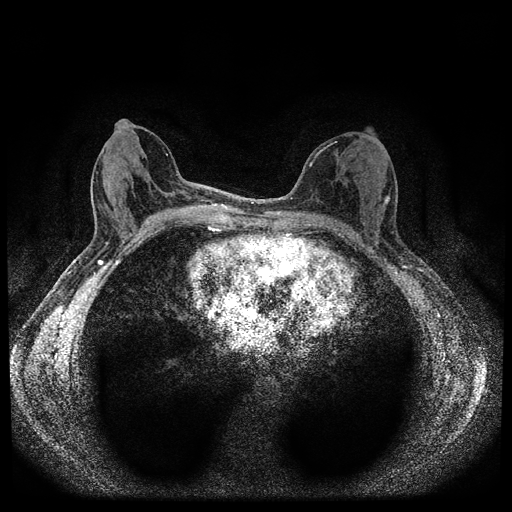
Breast MRI (dynamic contrast-enhanced, multi-phase), one axial slice. Slice 45 of 112 in the series (ordered by position). Dynamic contrast-enhanced series, time point 2 of 5 at this slice position (early post-contrast). 1.5 T. TE 2.7 ms, TR 5.4 ms. 2 mm slice thickness. 512 × 512 image matrix. Patient: female, 61 years.
Annotated regions visible in this slice (semi-automatic segmentation, software-assisted and operator-edited):
- breast lesion (labelled 'tumour' in the annotation; benign lesions carry a separate 'benign' label): bounding box (x1, y1, x2, y2) in pixels: (383, 195, 391, 204)
- breast lesion (labelled benign in the annotation): (334, 148, 339, 160)